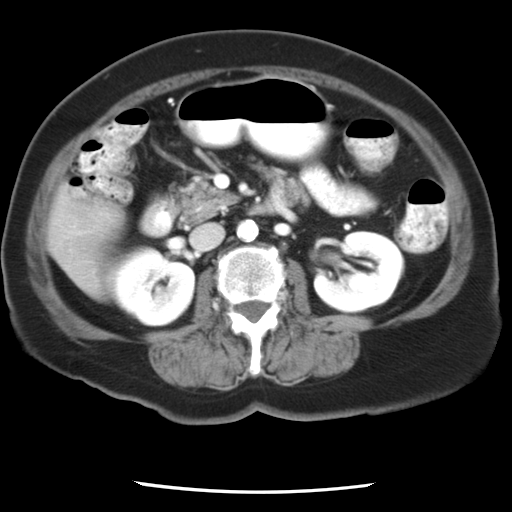
Contrast-enhanced abdominal CT, one axial slice. Position 7 of 24 along the scan axis. Reconstruction kernel STANDARD. Intravenous contrast given. Soft-tissue window (W 400 / L 40 HU). 512 × 512 image matrix. Female patient, age 71 years. Case-level facts recorded for this patient, not image findings: diagnosis: colorectal cancer liver metastases, imaged before liver resection; multiple liver metastases: no; largest metastasis: 4.3 cm.
Outlined on this slice (expert manual segmentation):
- liver: bounding box <48,193,123,297> (left, top, right, bottom; pixels)
- planned liver remnant (the part of the liver to remain after resection): <49,194,123,298>